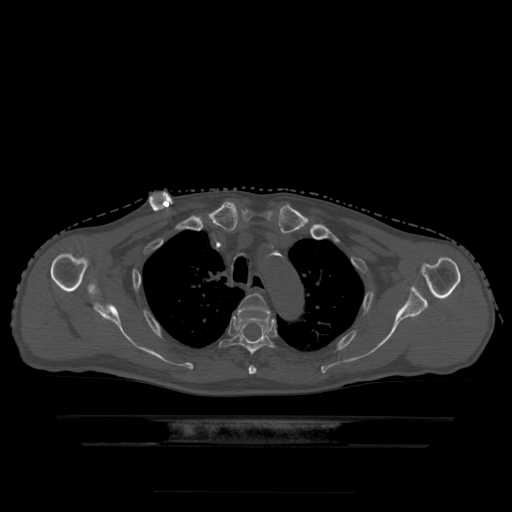
CT including the spine, one axial slice; bone window (W 1800 / L 400 HU); 1.25 mm slice thickness; 512 × 512 image matrix, field of view 436 × 436 mm. Patient age 68 years. Case-level facts recorded for this patient, not image findings: primary cancer: urothelial.
Structures marked on this image (semi-automatic segmentation, software-assisted and operator-edited):
- T3 vertebra: bounding box (x1, y1, x2, y2) in pixels: (238, 294, 270, 375)
- T4 vertebra: (220, 314, 274, 356)